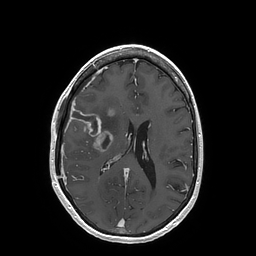
Brain MRI from a brain-tumour surgery series, one axial slice. Slice 72 of 202 in the series (ordered by position). T1-weighted post-contrast. 1 mm slice thickness. 256 × 256 image matrix, field of view 250 × 250 mm. From the clinical record (not read from this slice): histopathology: Glioblastoma; WHO grade: 4; IDH mutation: no; tumour location: Right Insular.
Structures marked on this image (expert manual segmentation):
- tumour: box from (x=70, y=108) to (x=113, y=152) px